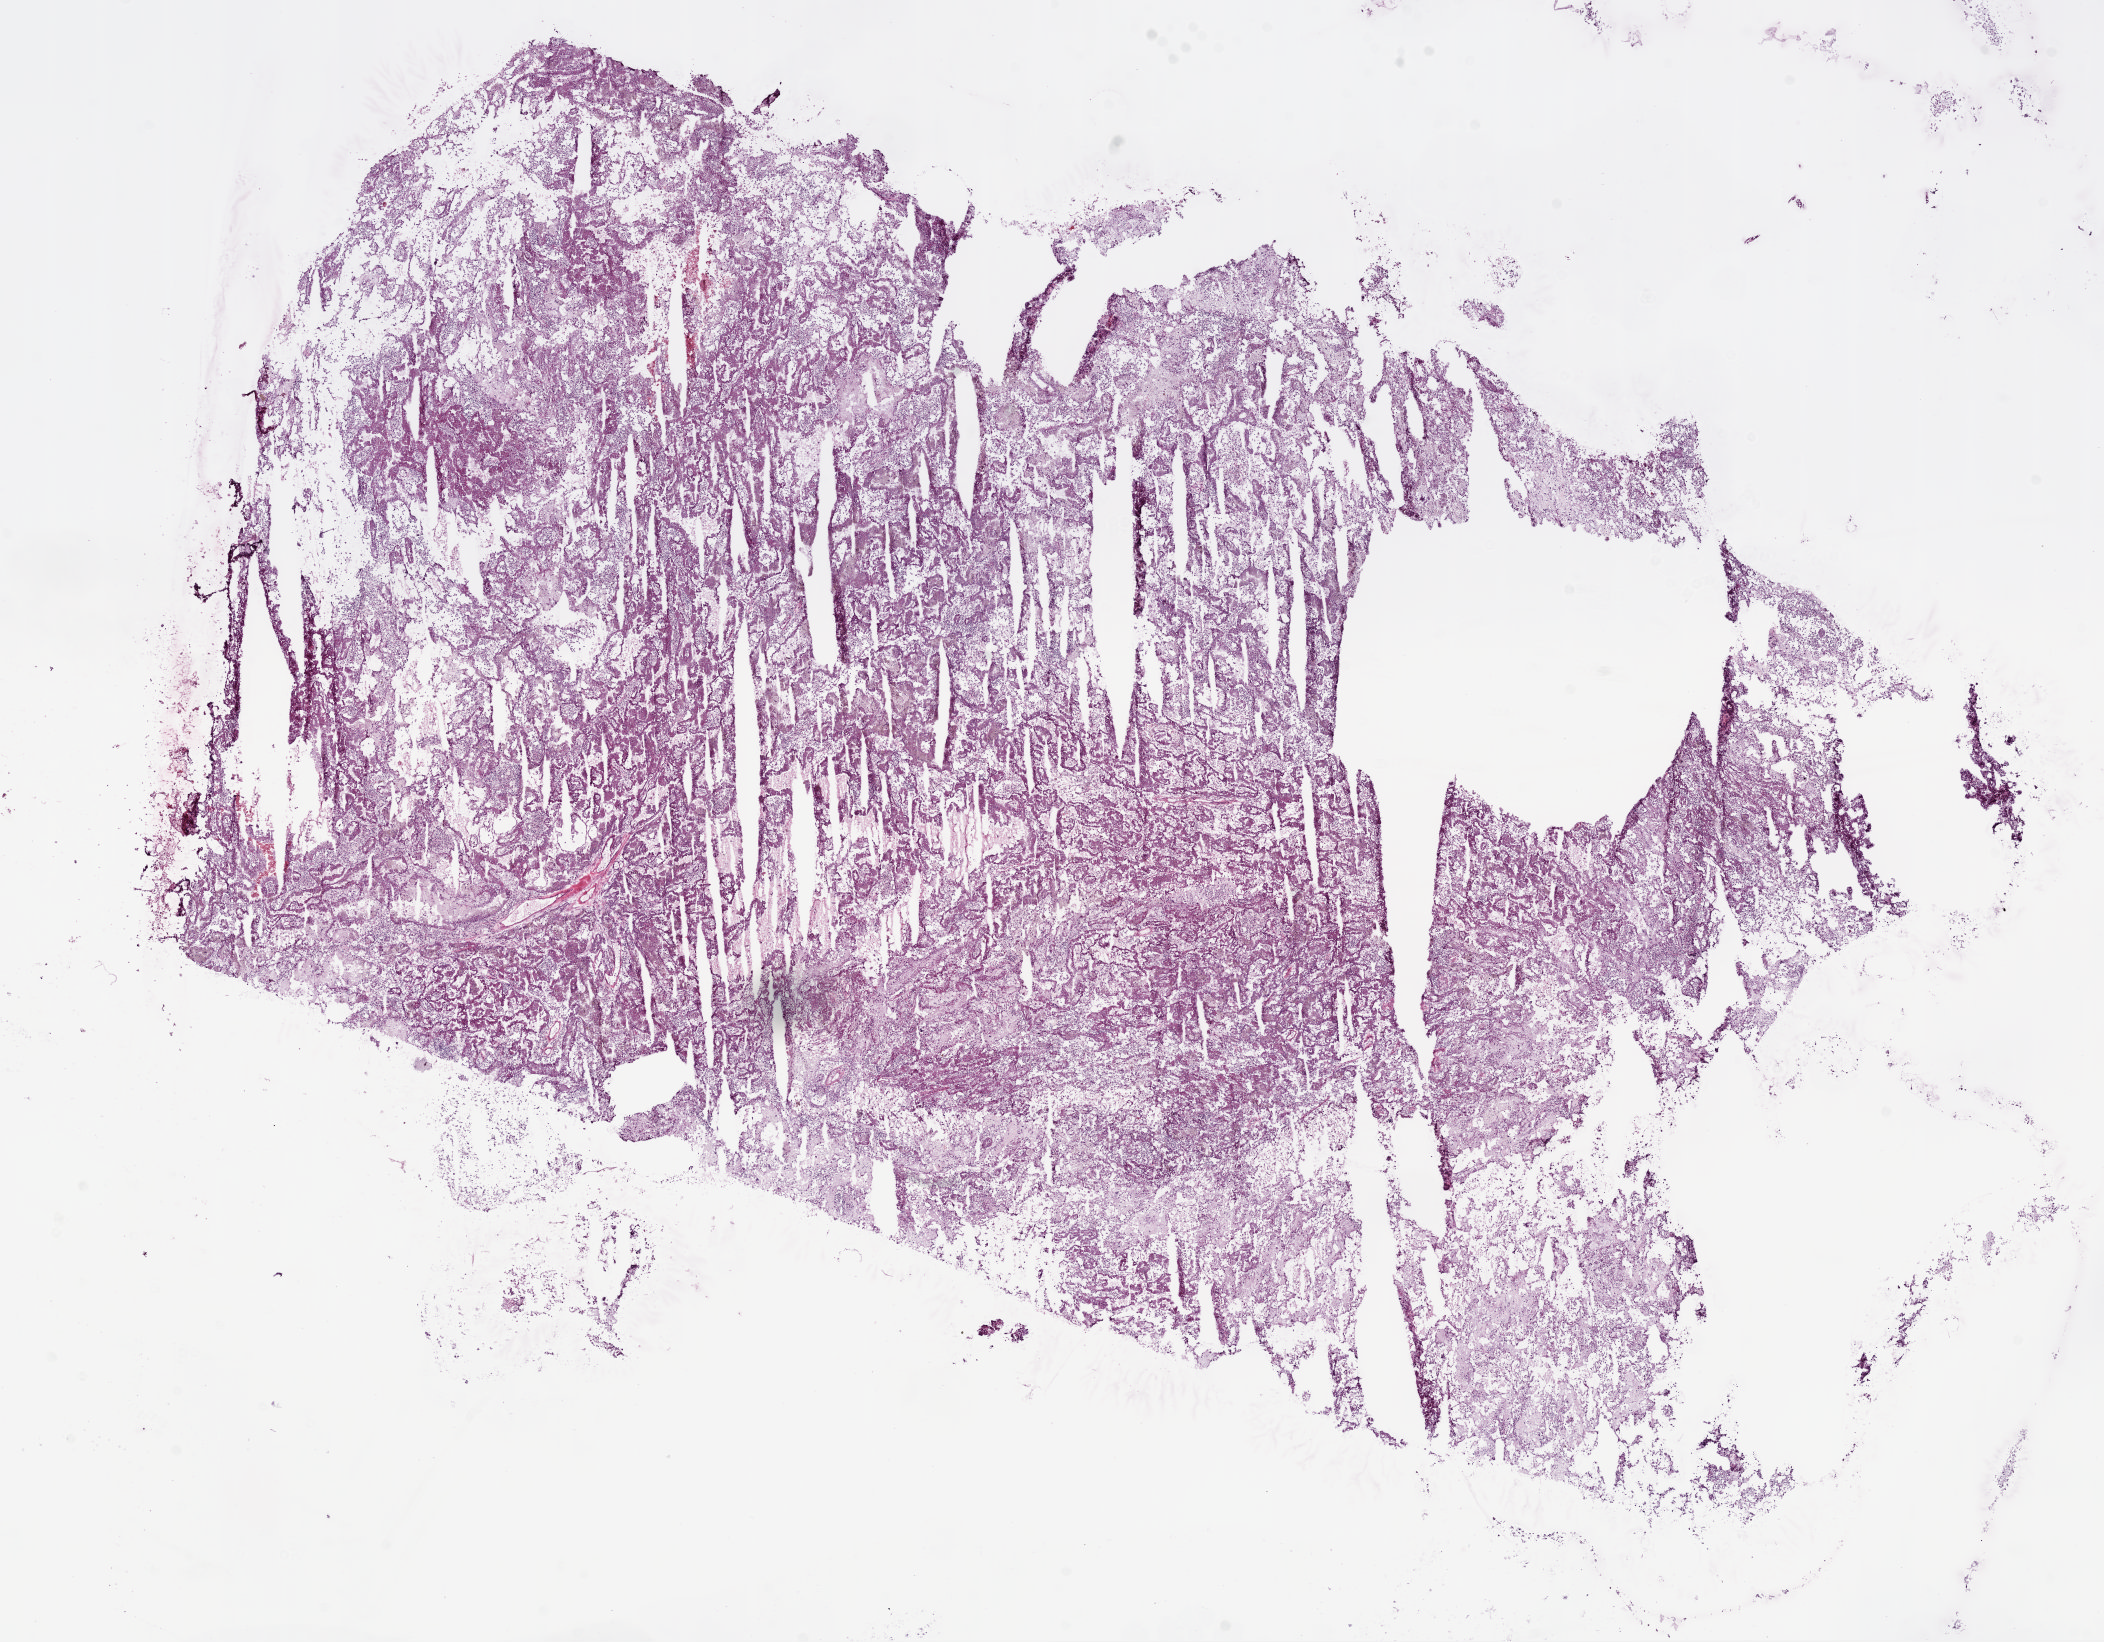
H&E-stained whole-slide image — a low-resolution overview of the entire scanned area, about 16.9 x 13.2 mm, frozen section from the bottom of the tissue portion, kidney, primary tumour sample. Male, age 73 years at initial diagnosis. Composition of this section per pathologist review: tumour cells 95%, tumour nuclei 60%, normal cells 0%, stromal cells 5%, necrosis 0%.
• histologic diagnosis: Papillary adenocarcinoma, NOS
• AJCC pathologic stage: III (7th edition)
• laterality: right